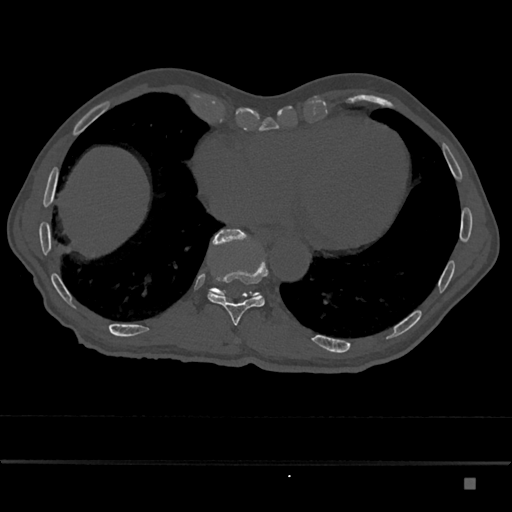
CT including the spine, one axial slice; slice 729 of 797 in the series (ordered by position); reconstruction kernel Br40s/3; bone window (W 1800 / L 400 HU); 0.5 mm slice thickness; 512 × 512 image matrix, field of view 390 × 390 mm. Patient: male, 72 years. From the clinical record (not read from this slice): primary cancer: prostate.
Structures marked on this image (semi-automatic segmentation, software-assisted and operator-edited):
- T10 vertebra: bounding box (x1, y1, x2, y2) in pixels: (208, 262, 268, 326)
- T11 vertebra: (209, 229, 260, 300)